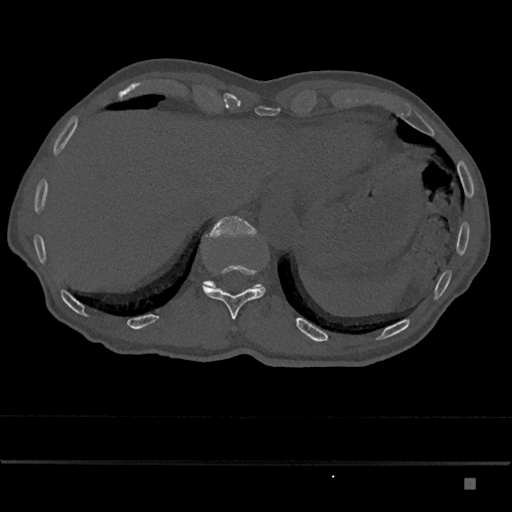
CT including the spine, one axial slice. Slice 663 of 797 in the series (ordered by position). Bone window (W 1800 / L 400 HU). 0.5 mm slice thickness. 512 × 512 image matrix. Male patient, age 72 years. Case-level facts recorded for this patient, not image findings: primary cancer: prostate.
Outlined on this slice (semi-automatic segmentation, software-assisted and operator-edited):
- T11 vertebra: box from (x=202, y=265) to (x=266, y=320) px
- T12 vertebra: (x=203, y=216)–(x=263, y=288)